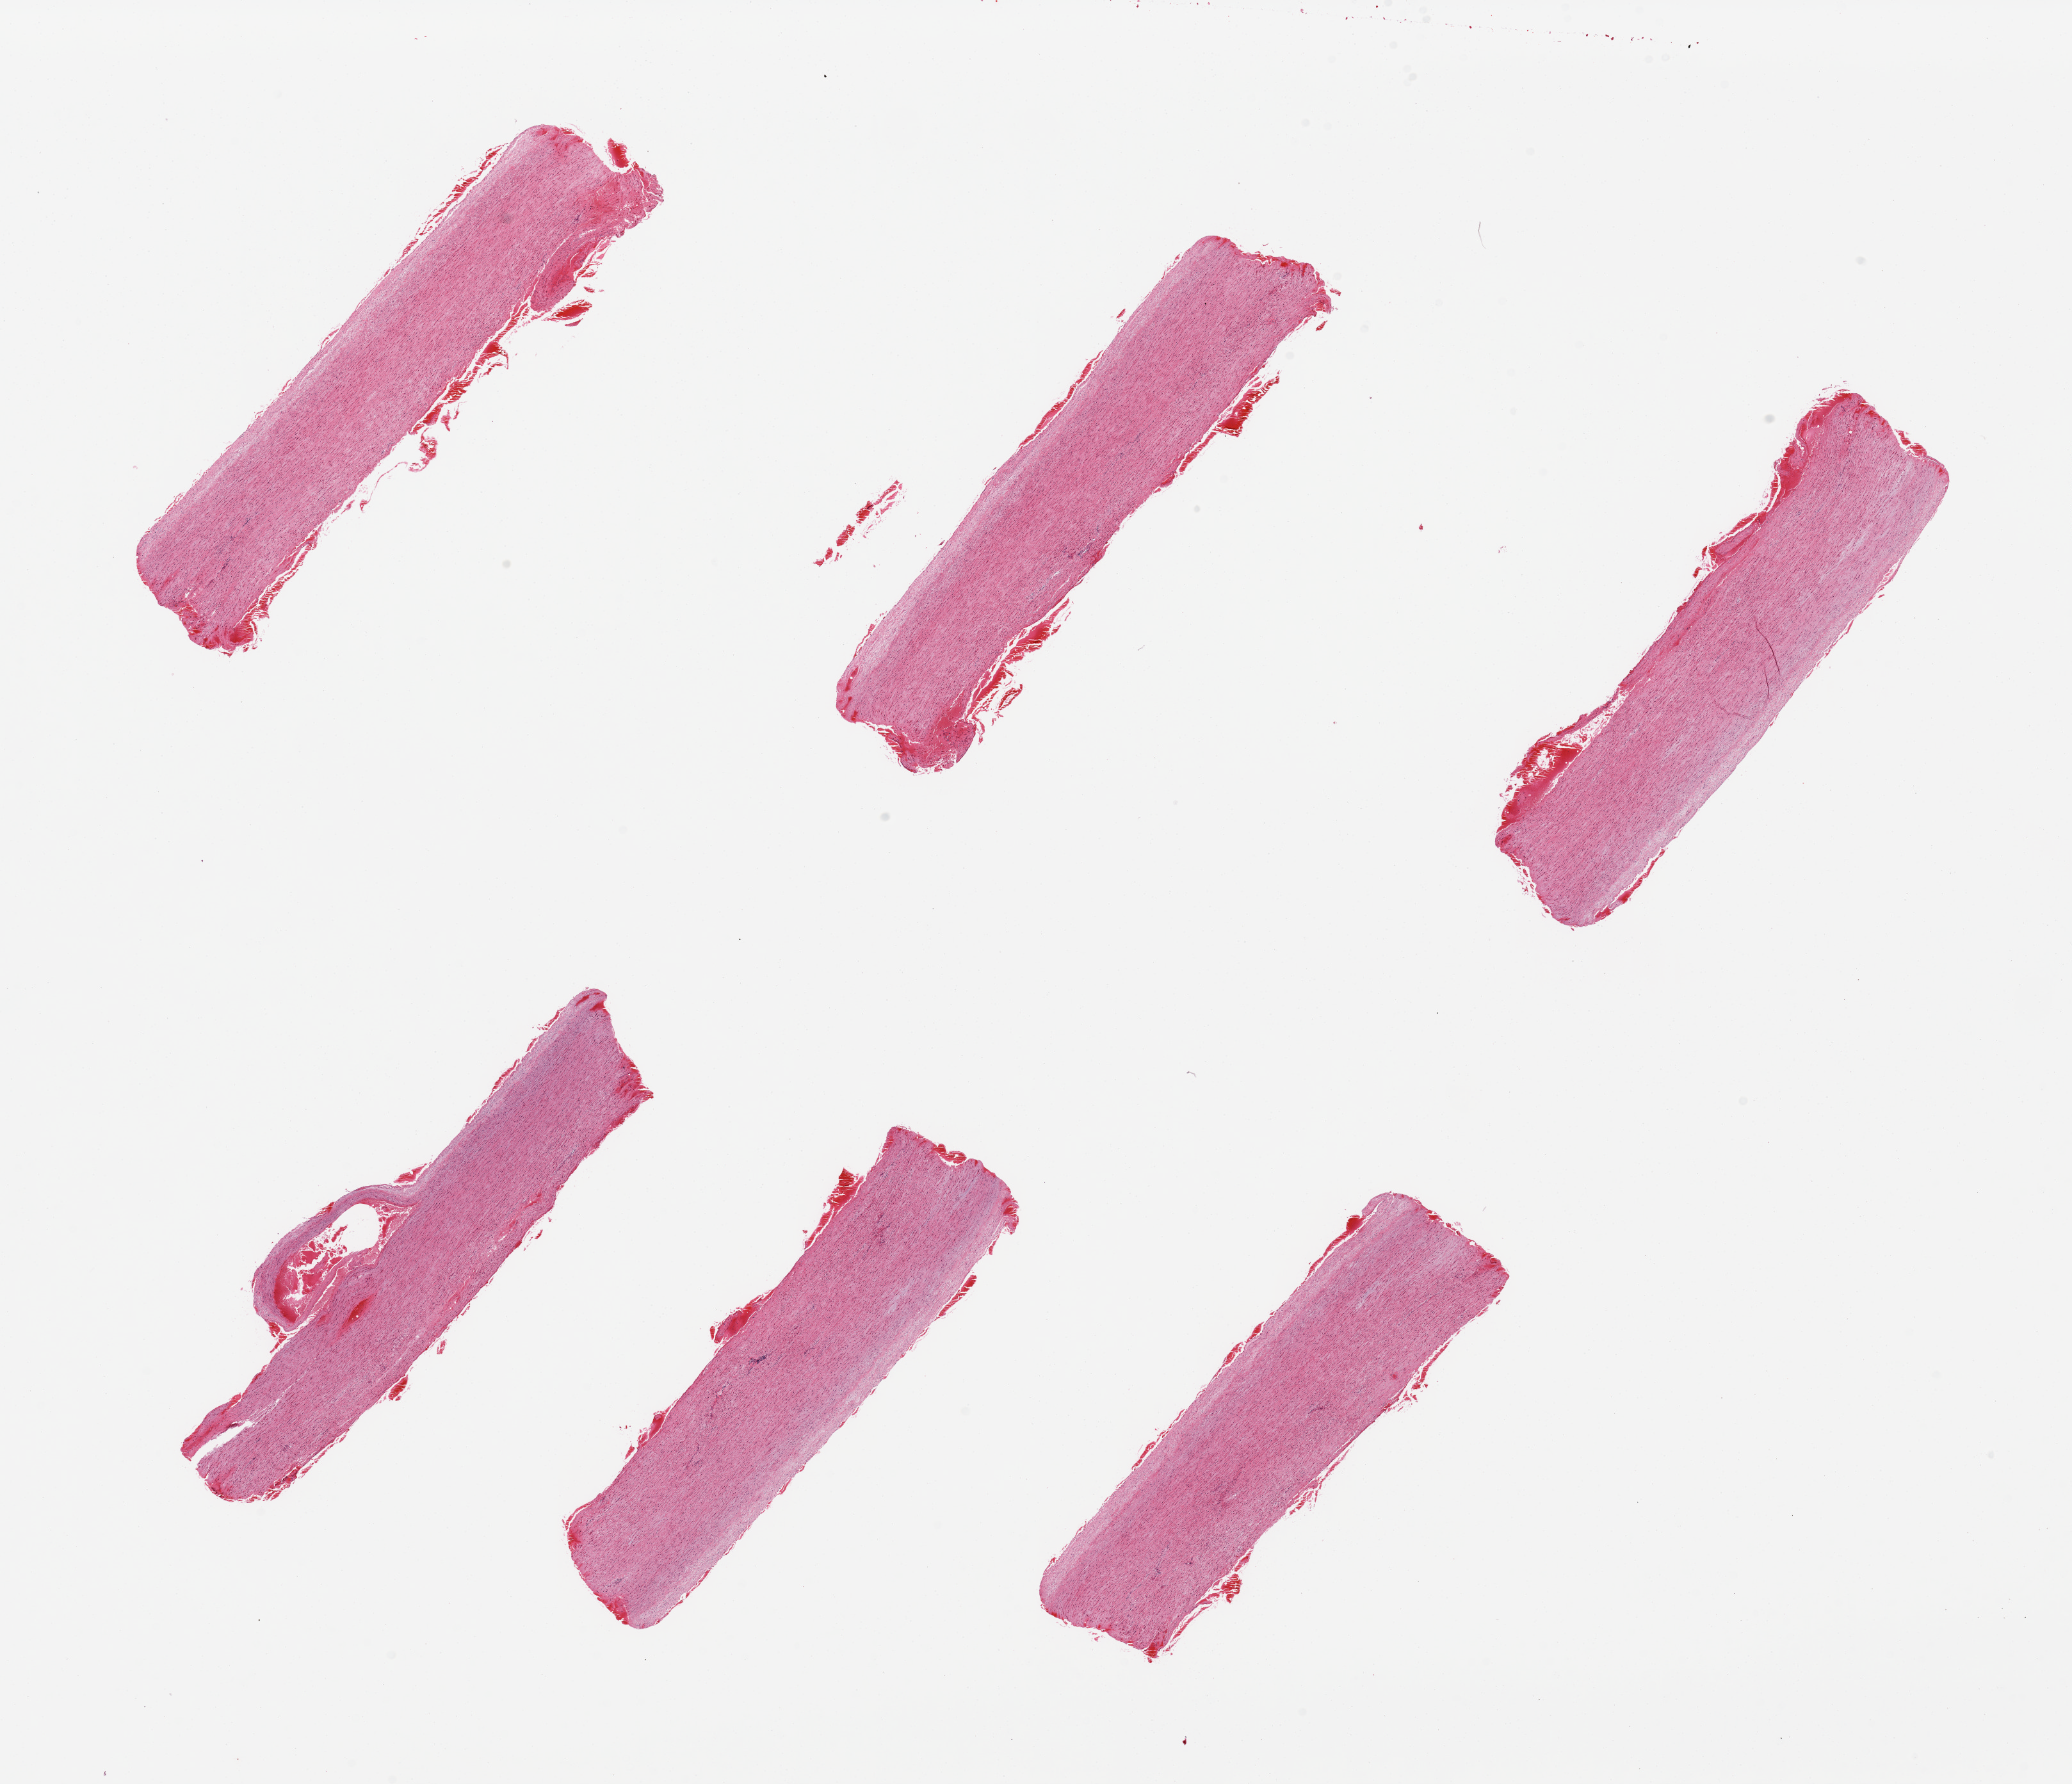
Whole-slide image, hematoxylin and eosin (H&E) stain, brightfield, low-resolution overview of the scanned area, about 25.6 x 22.0 mm (acquisition: 20x scan); PAXgene-fixed, paraffin-embedded tissue; target tissue: aorta; tissue donor sample. Donor sex: male.
* reviewer comment on this tissue sample: 6 pieces